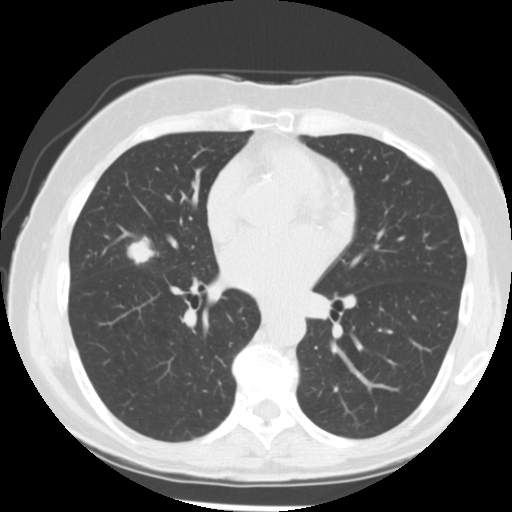
Chest CT (low-dose screening protocol), one axial image; first (baseline) screen; lung window (W 1500 / L -600 HU); 2.5 mm slice thickness. Female, age 66 years at enrolment.
Lesion marked by an expert reader, bounding box (x1, y1, x2, y2) in pixels: (121, 235, 163, 269). Reader record for this screening exam (exam-level; its link to the box is not recorded): non-calcified nodule or mass ≥4 mm, right middle lobe, 15 × 13 mm, poorly defined margins, soft tissue attenuation. Lung cancer was diagnosed 27 days after this screen: adenocarcinoma, NOS, right middle lobe, undifferentiated (G4), stage IIIA (AJCC 6th edition), 18 mm at pathology.